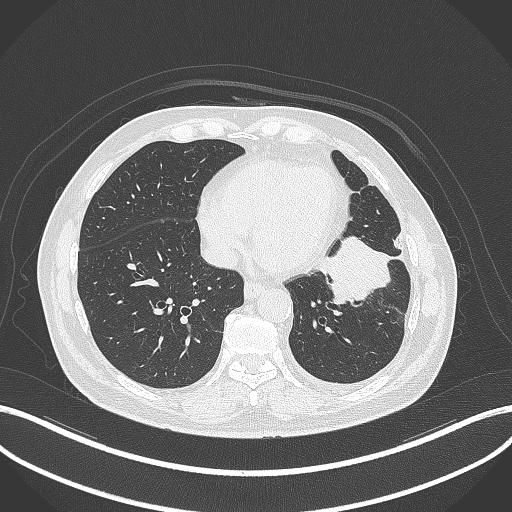
Chest CT, one axial slice; slice 118 of 230 in the series (ordered by position); reconstruction kernel B70f; lung window (W 1500 / L -600 HU); 1 mm slice thickness; 512 × 512 image matrix, field of view 400 × 400 mm. Male patient, age 68 years. From the clinical record (not read from this slice): clinical TNM (as recorded): T2b N0 M0.
Outlined on this slice (bounding box drawn by a radiologist):
- lung tumour (recorded histology: squamous cell carcinoma): box from (x=315, y=229) to (x=401, y=310) px